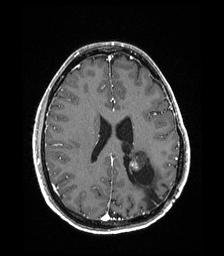
Brain MRI from a brain-tumour surgery series, one axial slice; position 78 of 192 along the scan axis; T1-weighted post-contrast; 224 × 256 image matrix, field of view 224 × 256 mm. From the clinical record (not read from this slice): histopathology: Low grade glioma; IDH mutation: no; tumour location: Left Parieto-Occipital Intraventricular.
Outlined on this slice (manually delineated by an expert):
- previous resection cavity: bounding box (x1, y1, x2, y2) in pixels: (128, 165, 162, 208)
- tumour: (129, 150, 150, 171)